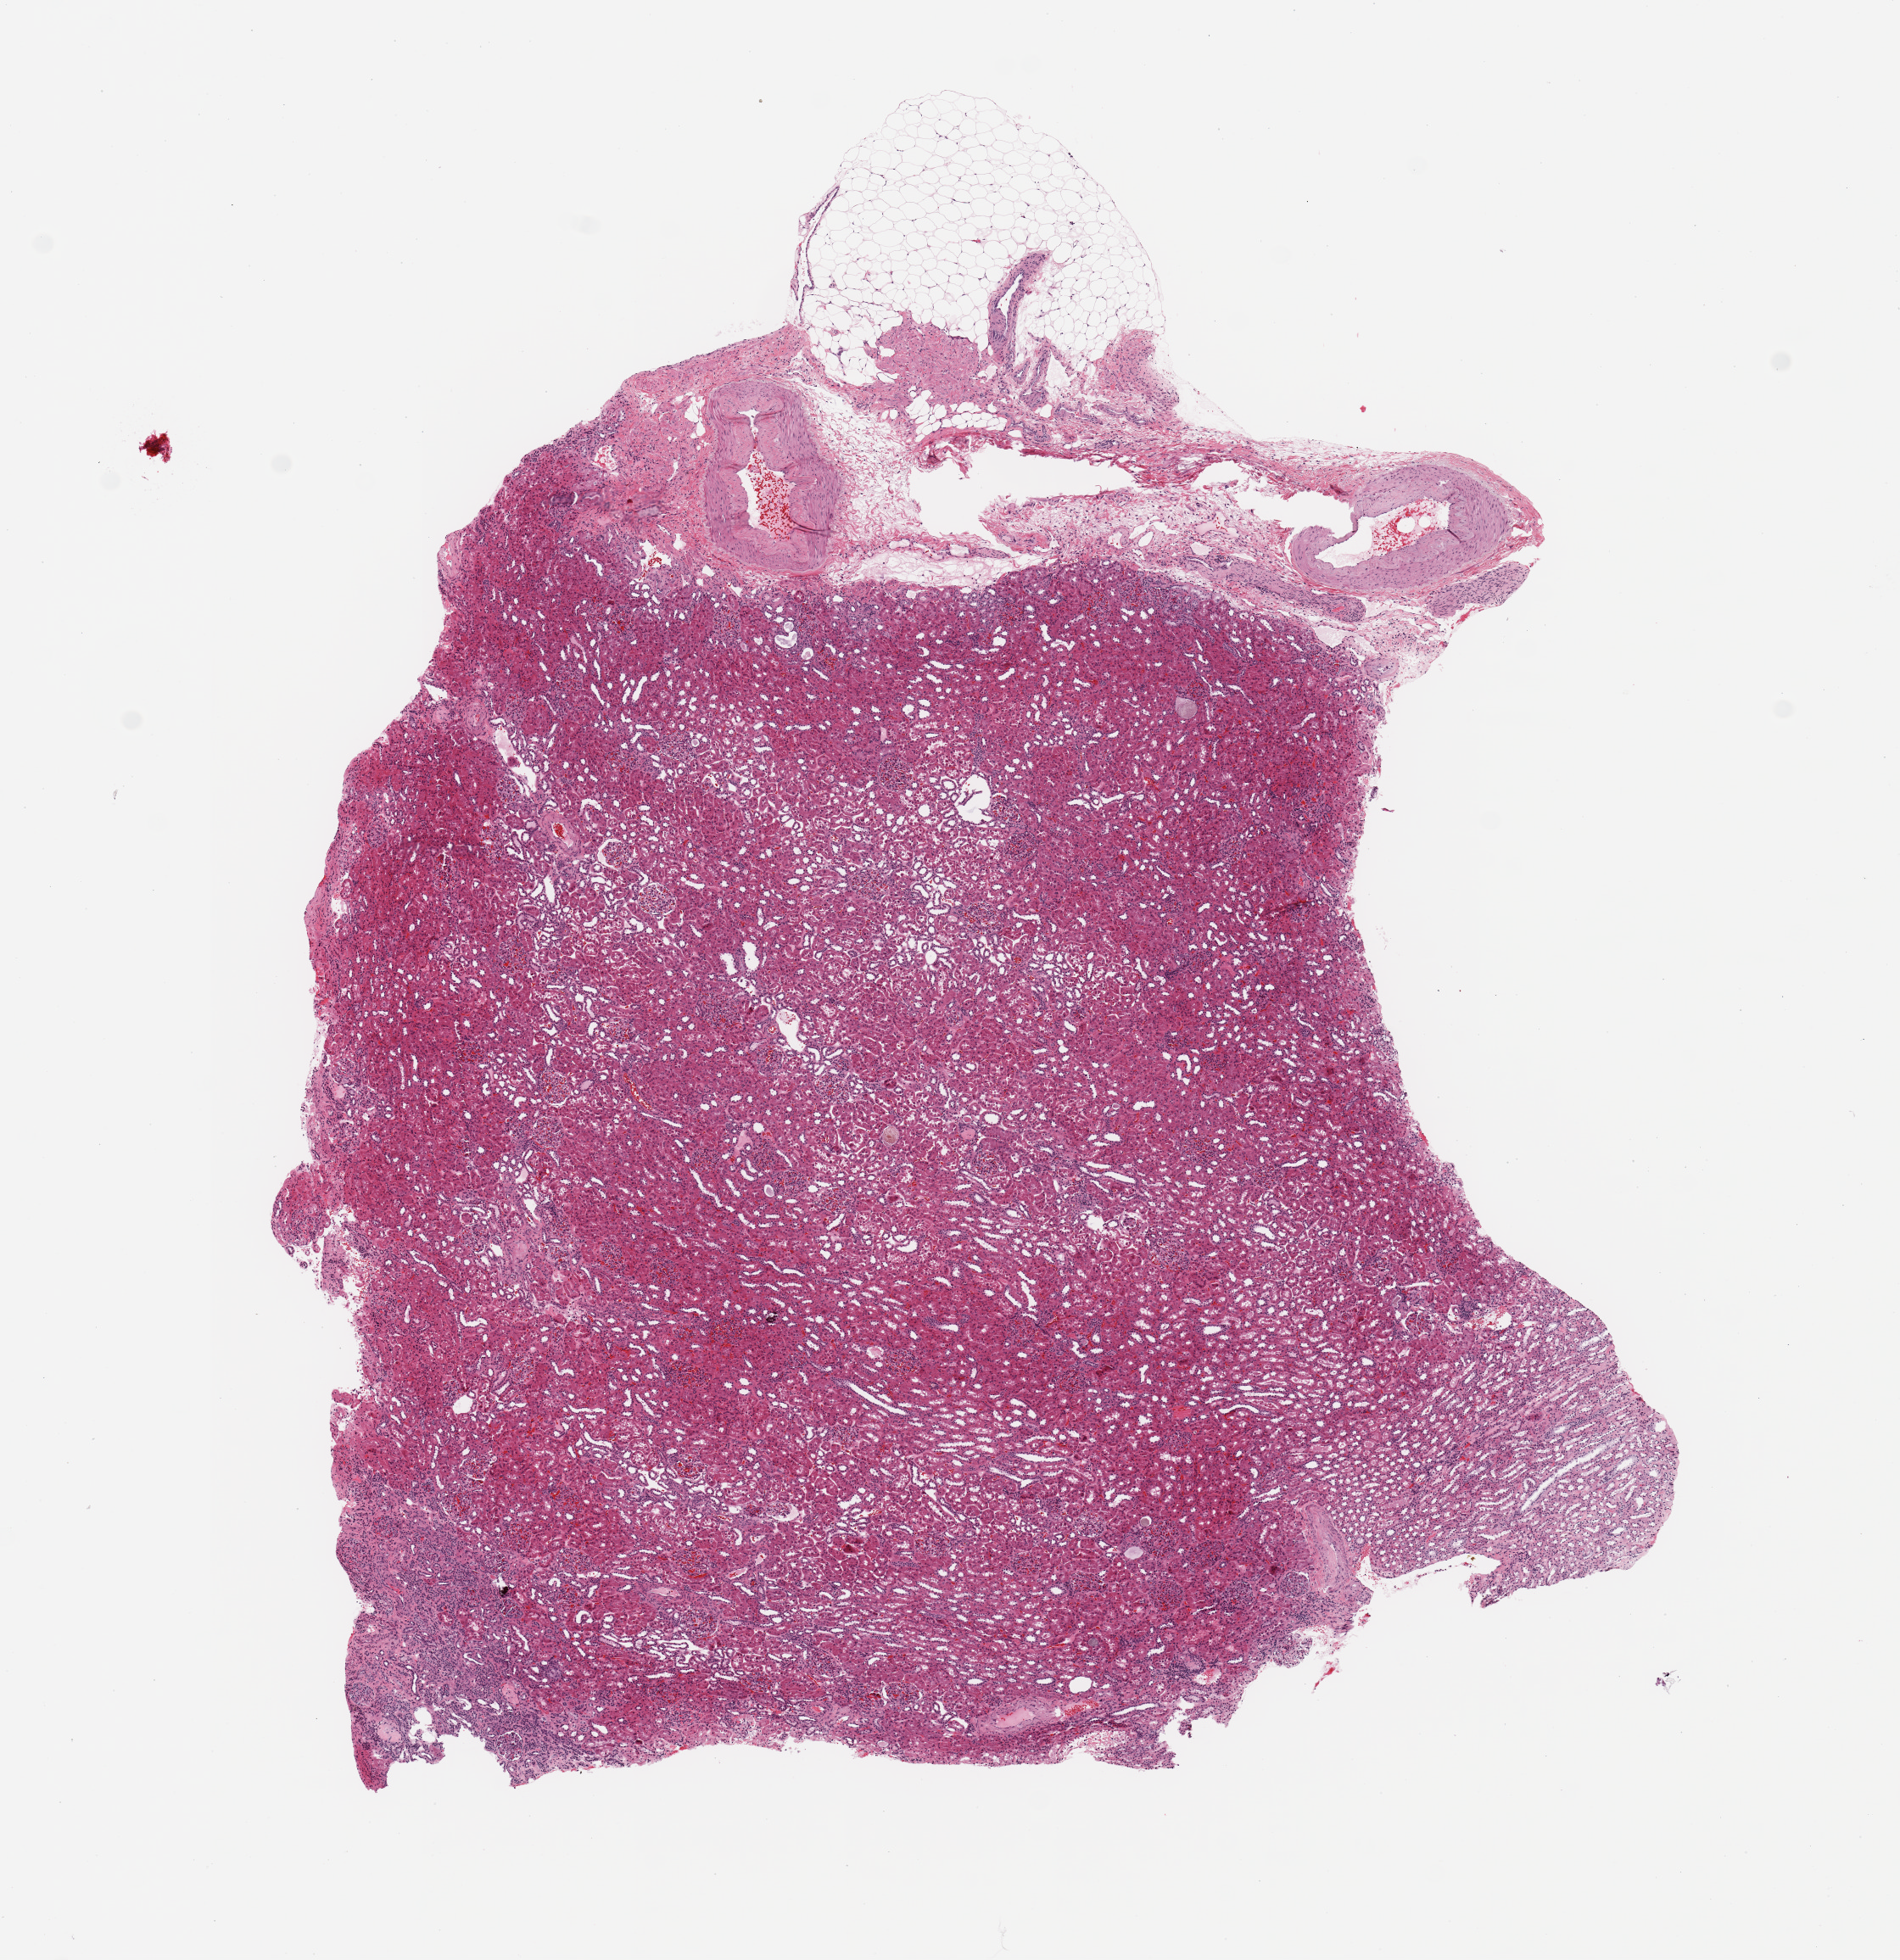
Whole-slide histology image, H&E-stained, shown as a low-resolution overview of the whole scanned area (about 8.9 x 9.1 mm, slide scanned at 20x); normal (non-tumour) tissue sample, sampled site: kidney. Female, 63 y/o.
This section: normal (non-tumour) tissue from the same patient. Patient diagnosis: Renal cell carcinoma, NOS.